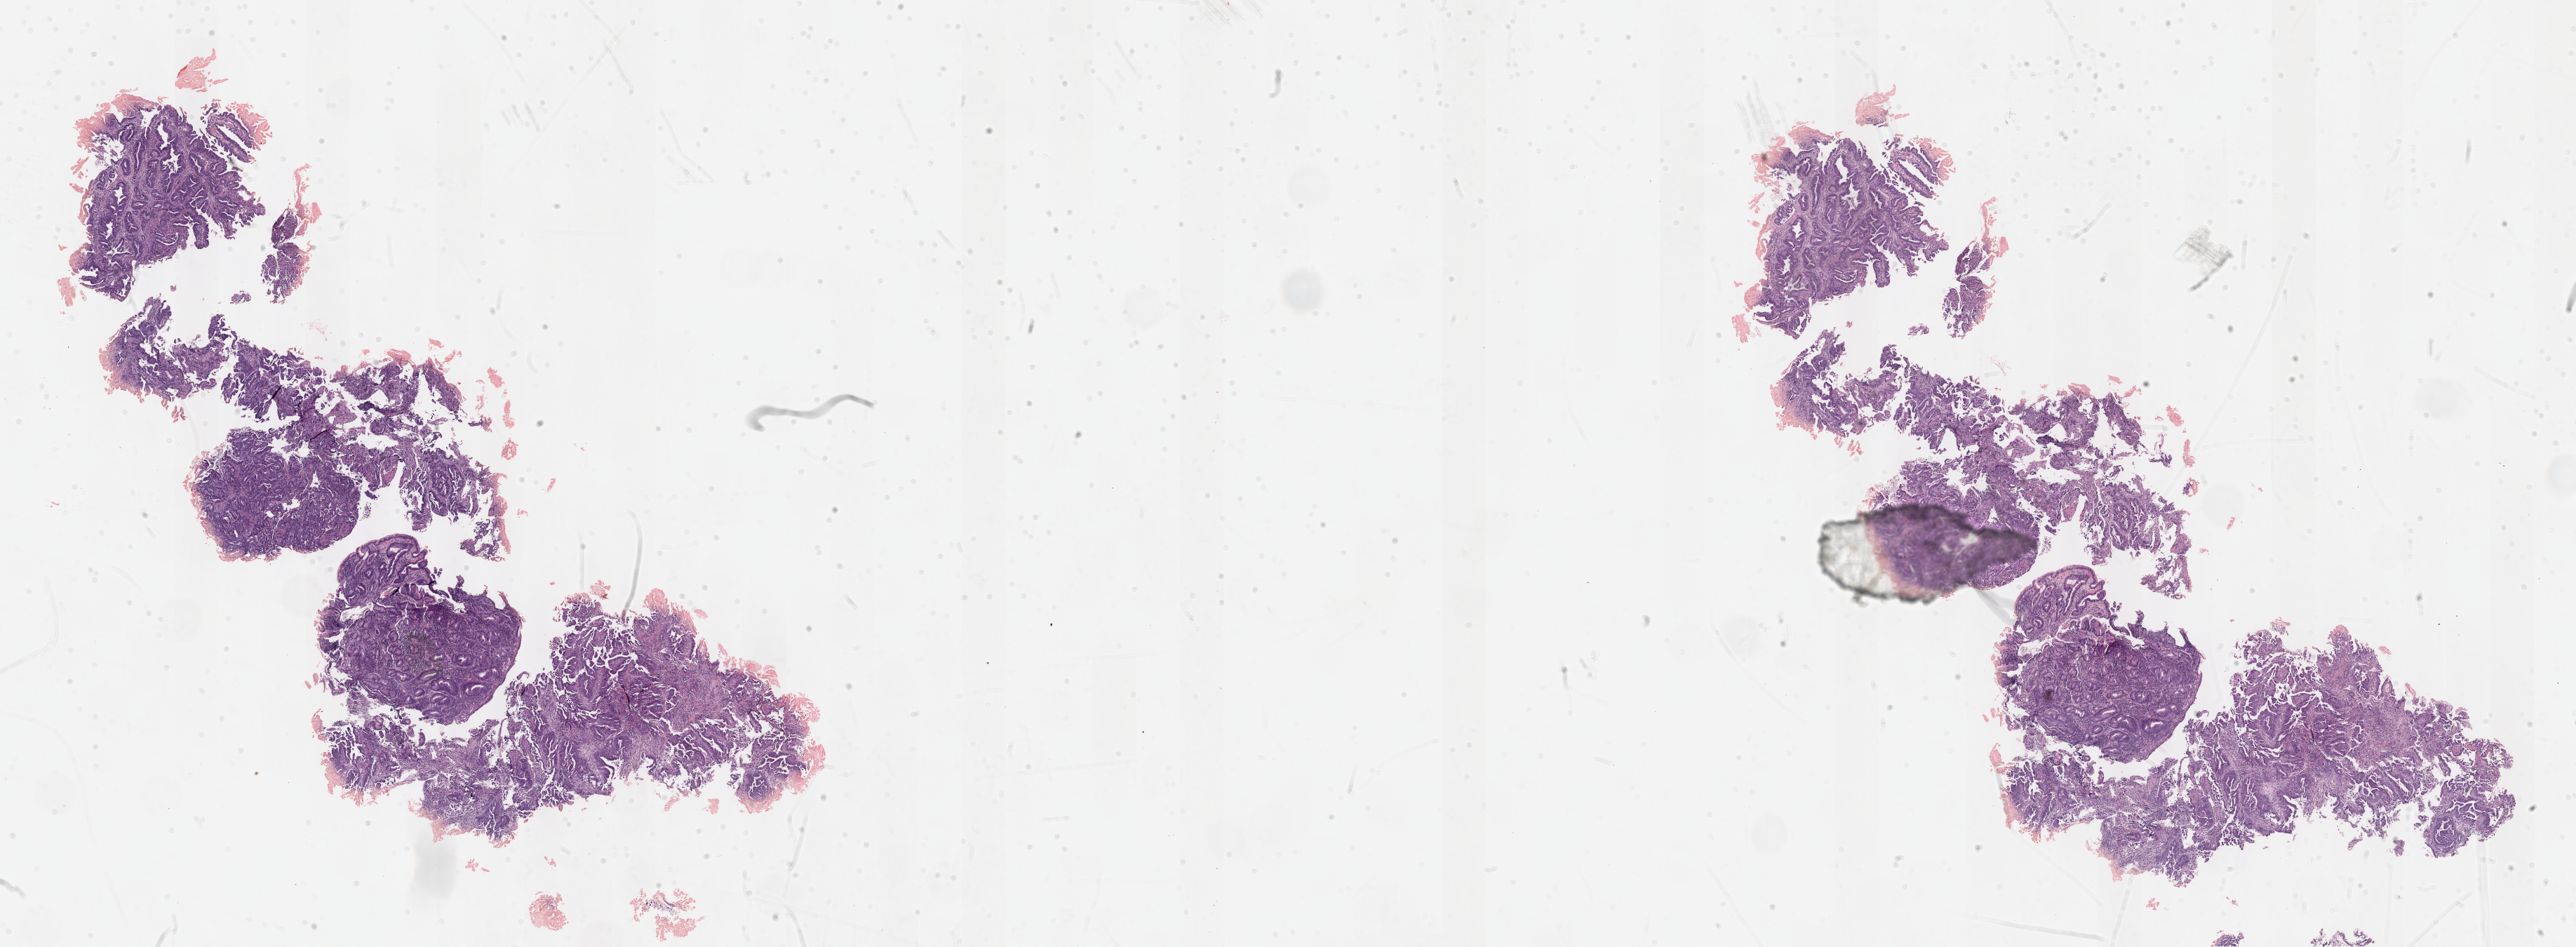
Digitized H&E tissue section (whole slide) — a low-resolution overview of the entire scanned area, about 29.7 x 10.9 mm. Formalin-fixed paraffin-embedded (FFPE) diagnostic section. Primary tumour sample from the esophagus. Male, age 60 years at initial diagnosis.
Diagnosis: Adenocarcinoma, NOS.